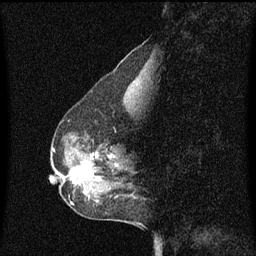
Breast MRI (dynamic contrast-enhanced), one sagittal slice. Position 22 of 60 along the scan axis. Dynamic contrast-enhanced series, image 2 of 3 at this slice position (ordered by acquisition). 1.5 T. TE 4.2 ms, TR 8.4 ms. 256 × 256 image matrix, field of view 200 × 200 mm. Female patient, age 50 years. Case-level facts recorded for this patient, not image findings: setting: breast cancer imaged before/during neoadjuvant chemotherapy; receptor status: HR-positive, HER2-negative.
Outlined on this slice (semi-automatically segmented with operator editing):
- analysis volume of interest (the breast-tissue region the enhancement analysis was run in; not a lesion): box from (x=61, y=144) to (x=128, y=189) px
- tumour enhancement mask (voxels above the 70 % enhancement threshold inside the analysis volume of interest): (x=70, y=154)–(x=113, y=185)